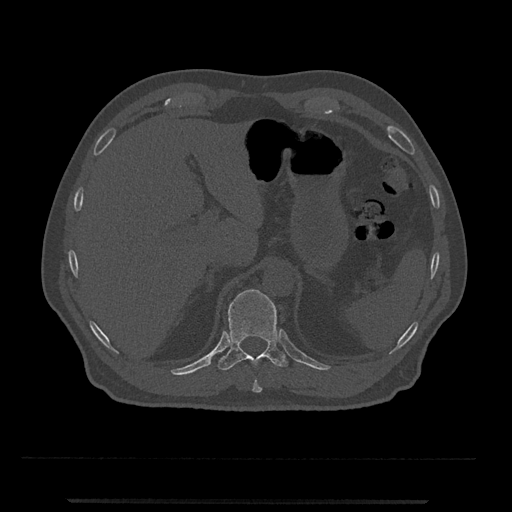
CT including the spine, one axial slice. Slice 475 of 797 in the series (ordered by position). 120 kVp. Bone window (W 1800 / L 400 HU). 0.5 mm slice thickness. 512 × 512 image matrix, field of view 419 × 419 mm. Patient: male, 63 years. Case-level facts recorded for this patient, not image findings: primary cancer: prostate.
Outlined on this slice (semi-automatic segmentation, software-assisted and operator-edited):
- T10 vertebra: bounding box (x1, y1, x2, y2) in pixels: (252, 380, 262, 393)
- T11 vertebra: (218, 289, 288, 370)